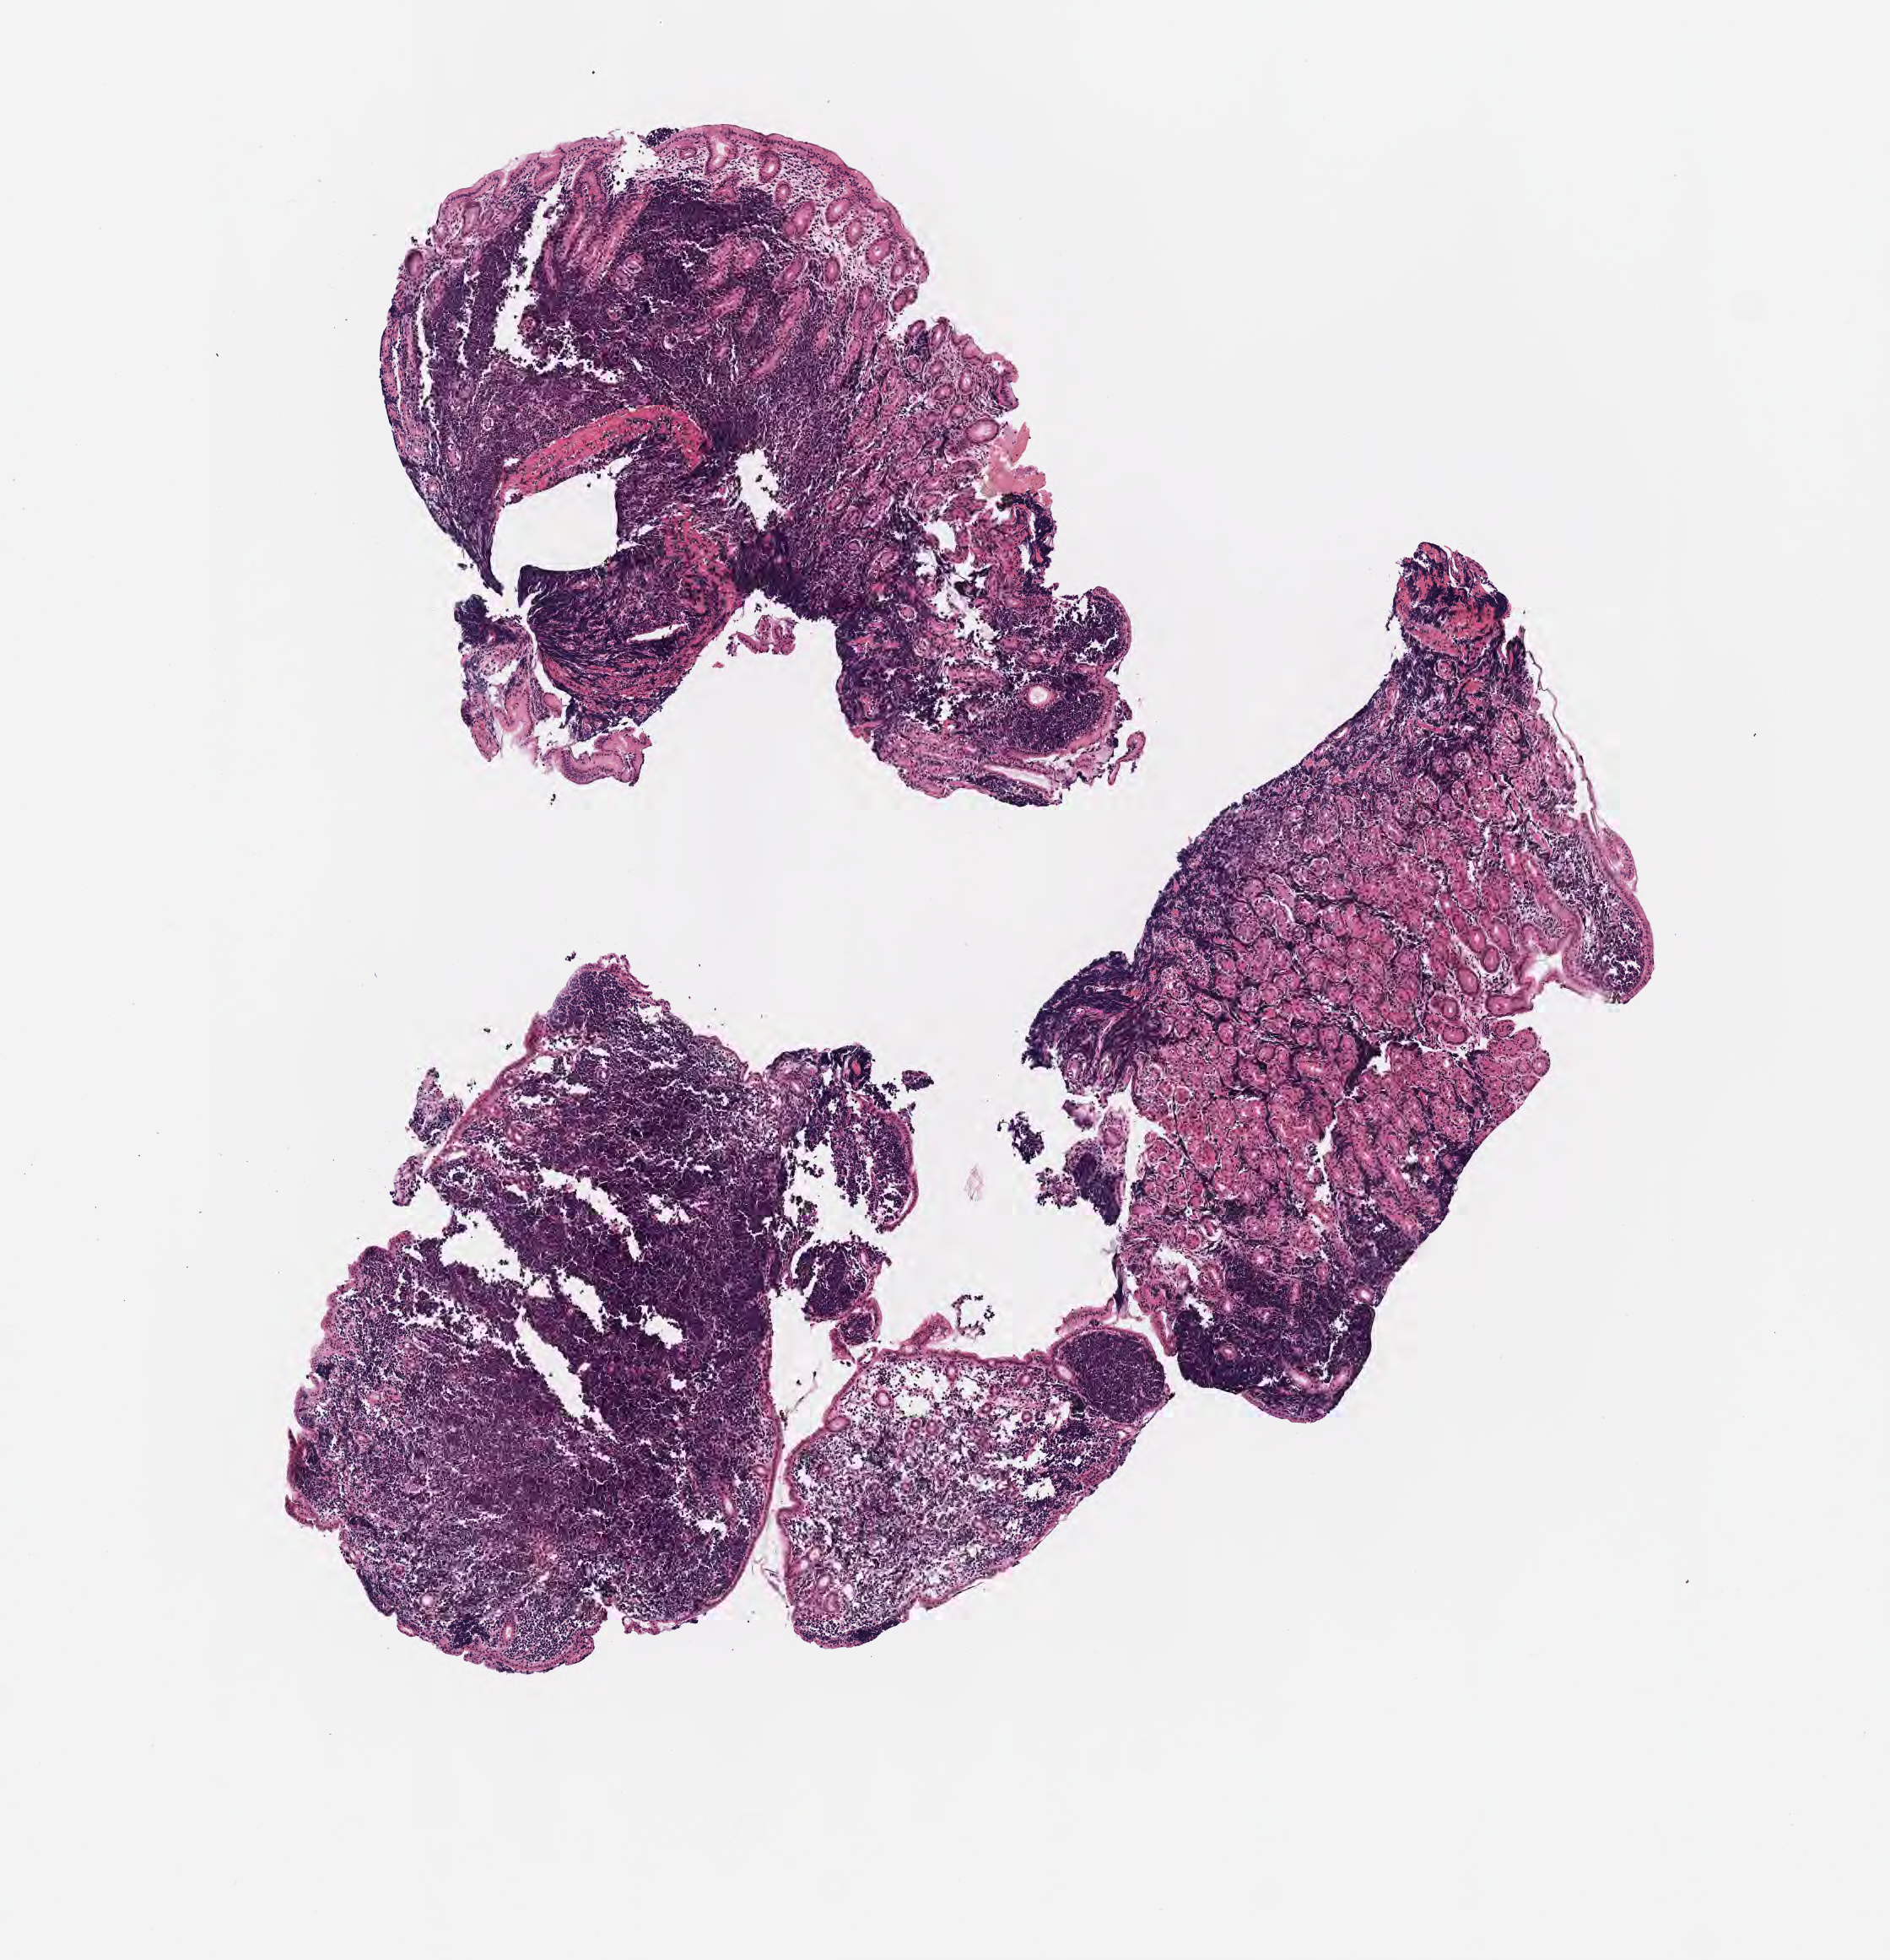
H&E whole-slide image, low-resolution overview of the scanned area, about 4.5 x 4.7 mm, specimen: tumor tissue. Patient female; aged 45.
Histologic diagnosis: Burkitt lymphoma, NOS.